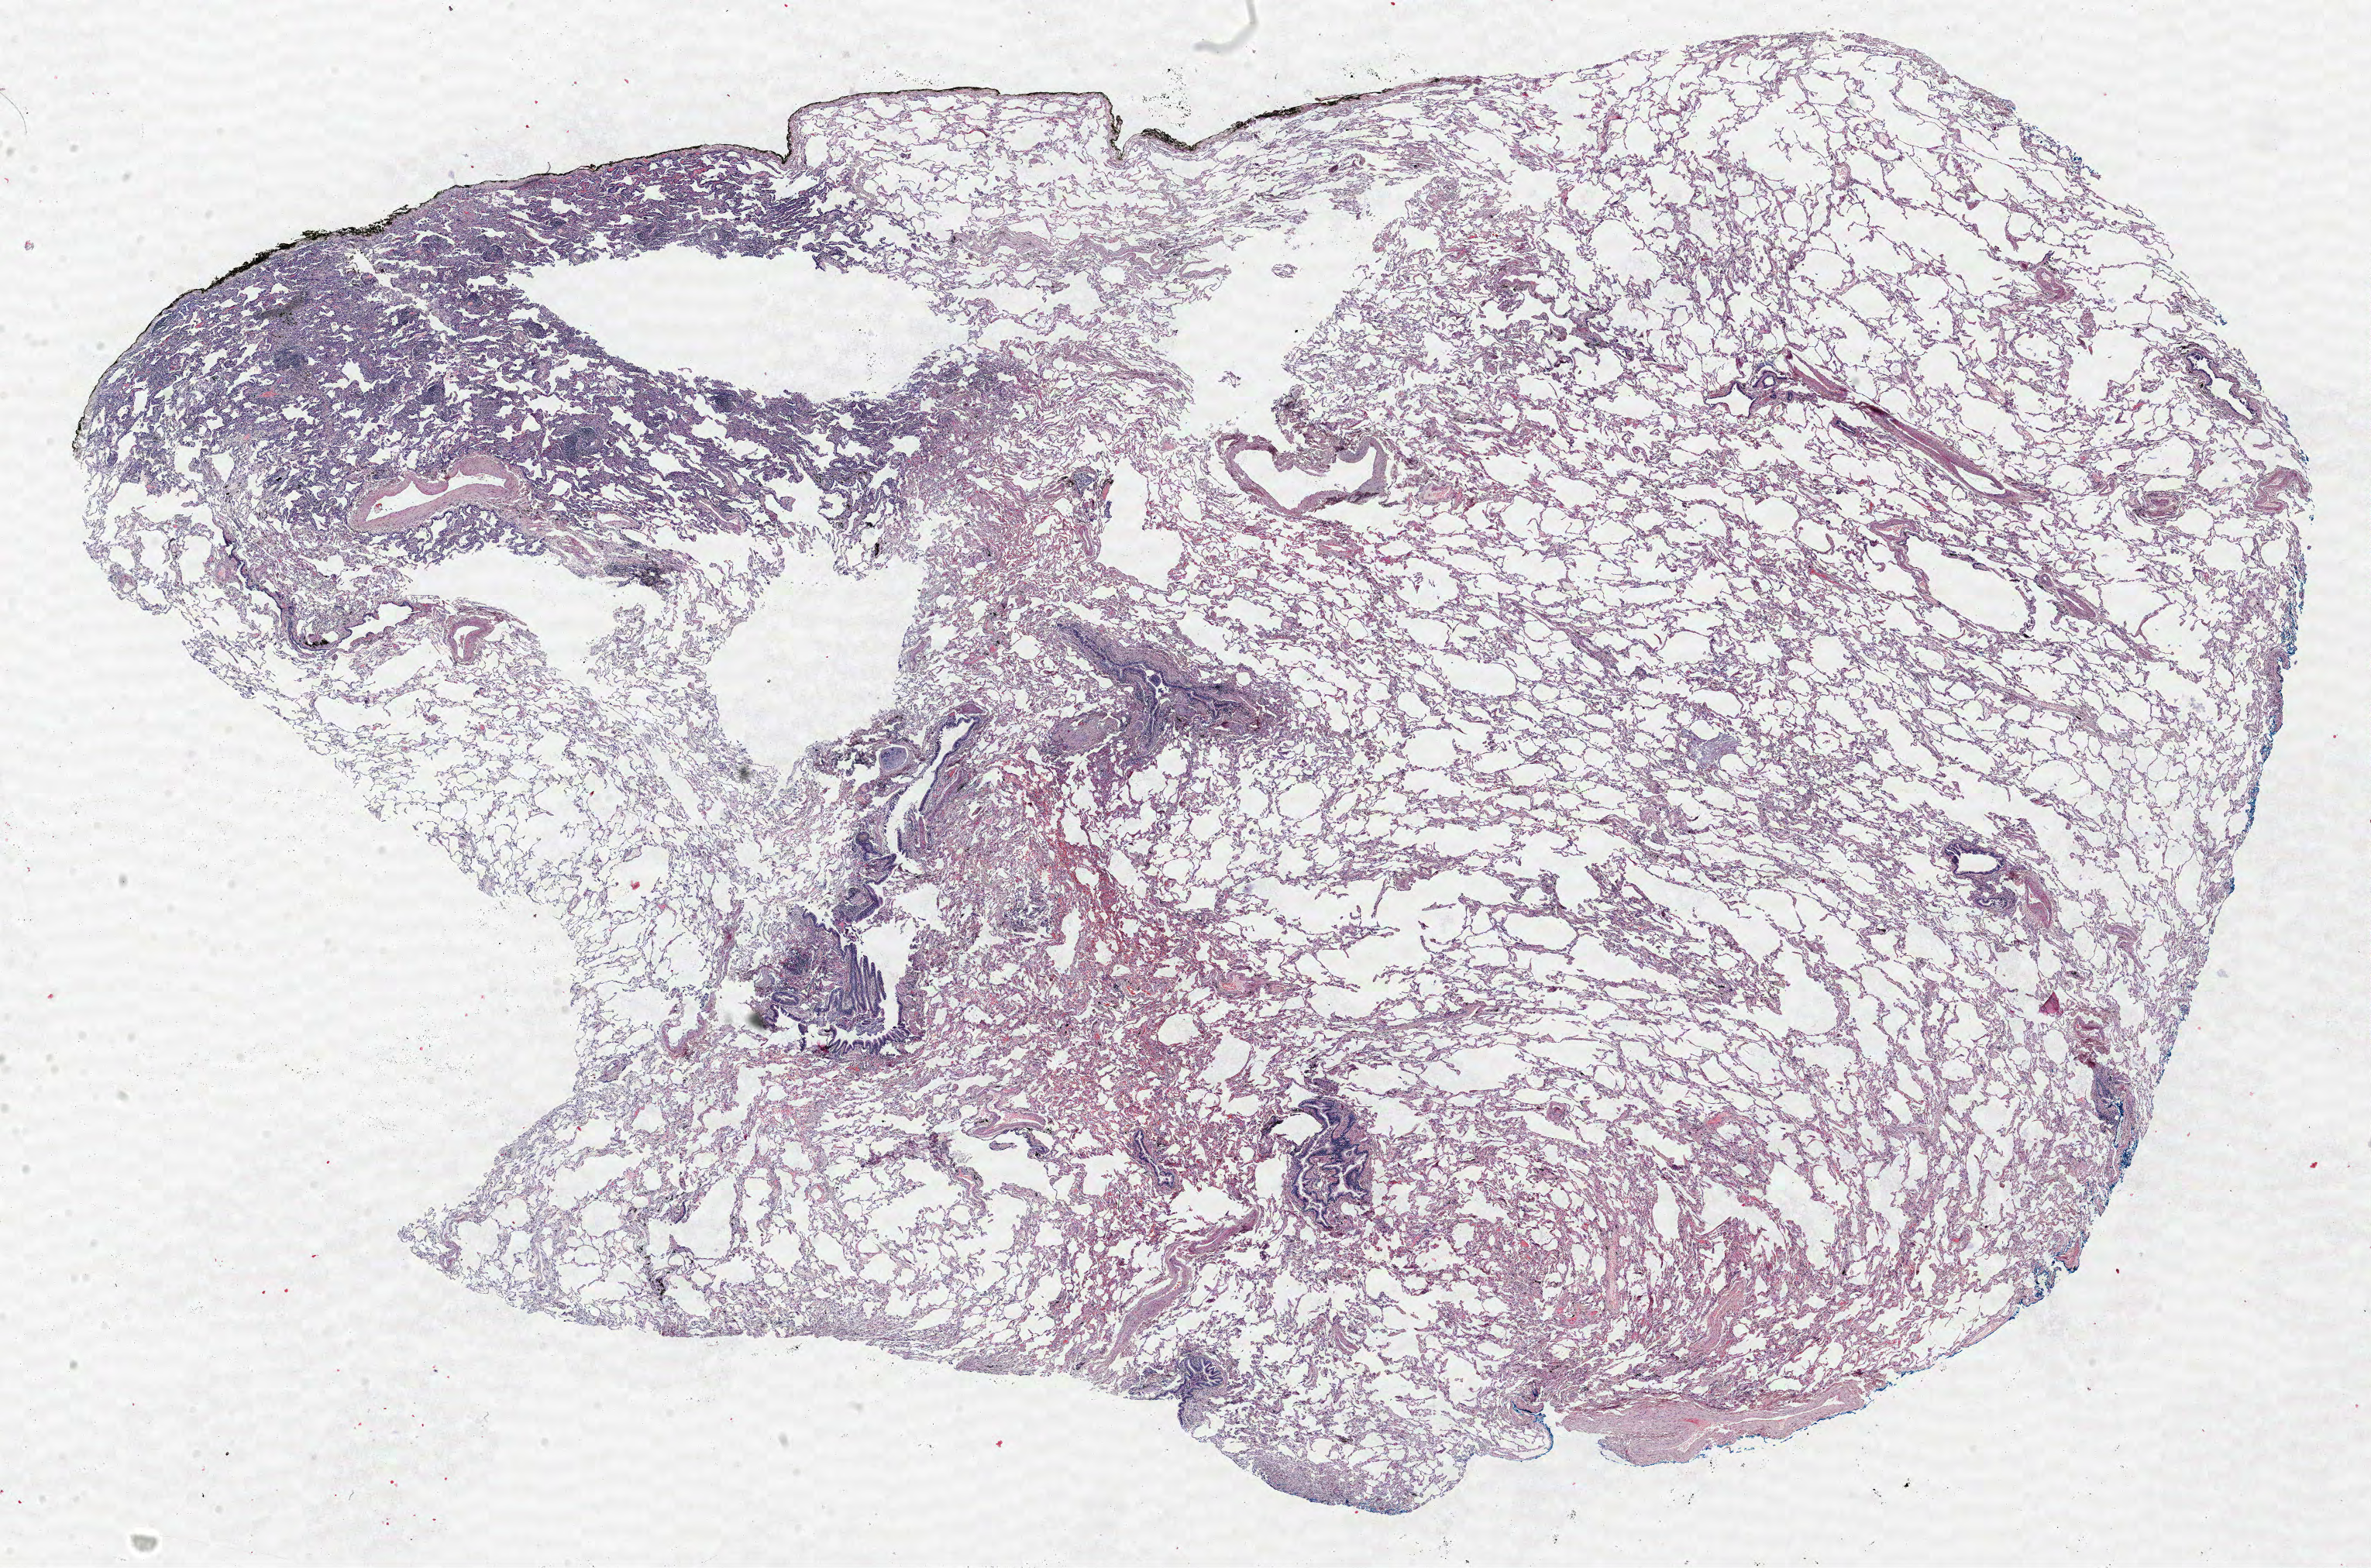
Whole-slide histology image, H&E-stained — shown as a low-resolution overview of the whole scanned area (about 24.5 x 16.2 mm), formalin-fixed paraffin-embedded (FFPE) section, lung tissue. Female, age 72 at enrolment. Grade: well differentiated (G1).
Primary tumour location (clinical record): right upper lobe. Participant's lung-cancer diagnosis: Bronchiolo-alveolar adenocarcinoma, NOS (ICD-O-3 8250/3). Tumour size (pathology): 23 mm. ICD-O-3 topography: upper lobe of lung (C34.1). Stage (AJCC 6th edition): IA.